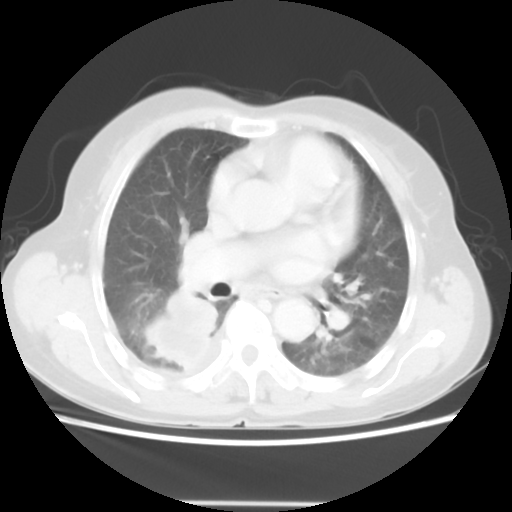
Chest CT, one axial slice. Slice 28 of 52 in the series (ordered by position). Reconstruction kernel STANDARD. 140 kVp. Lung window (W 1500 / L -600 HU). 5 mm slice thickness. 512 × 512 image matrix, field of view 337 × 337 mm. Female patient, age 67 years. Case-level facts recorded for this patient, not image findings: clinical TNM (as recorded): T3 N1 M1.
Annotated regions visible in this slice (rectangle marked by the reading radiologist):
- lung tumour (recorded histology: adenocarcinoma): bounding box (x1, y1, x2, y2) in pixels: (141, 285, 222, 371)